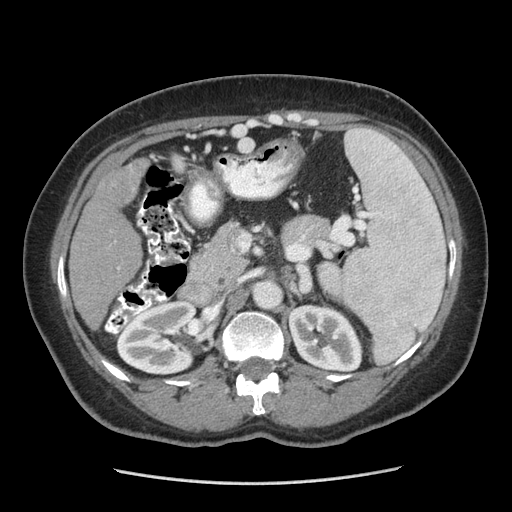
Contrast-enhanced abdominal CT (liver protocol), one axial slice; slice 138 of 185 in the series (ordered by position); 140 kVp; soft-tissue window (W 400 / L 40 HU); 2.5 mm slice thickness; 512 × 512 image matrix, field of view 360 × 360 mm. From the clinical record (not read from this slice): diagnosis: hepatocellular carcinoma (patient treated with transarterial chemoembolisation; whether this scan precedes or follows treatment is not stated here); TNM stage (as recorded): Stage-I; Child-Pugh class: A; tumour differentiation: poorly differentiated; tumour nodularity: uninodular.
Structures marked on this image (semi-automatic segmentation, software-assisted and operator-edited):
- liver parenchyma outside the tumour (the mass and vessels are separate outlines, so this box may not span the whole liver): box from (x=68, y=158) to (x=148, y=328) px
- mass: (x=97, y=161)–(x=143, y=211)